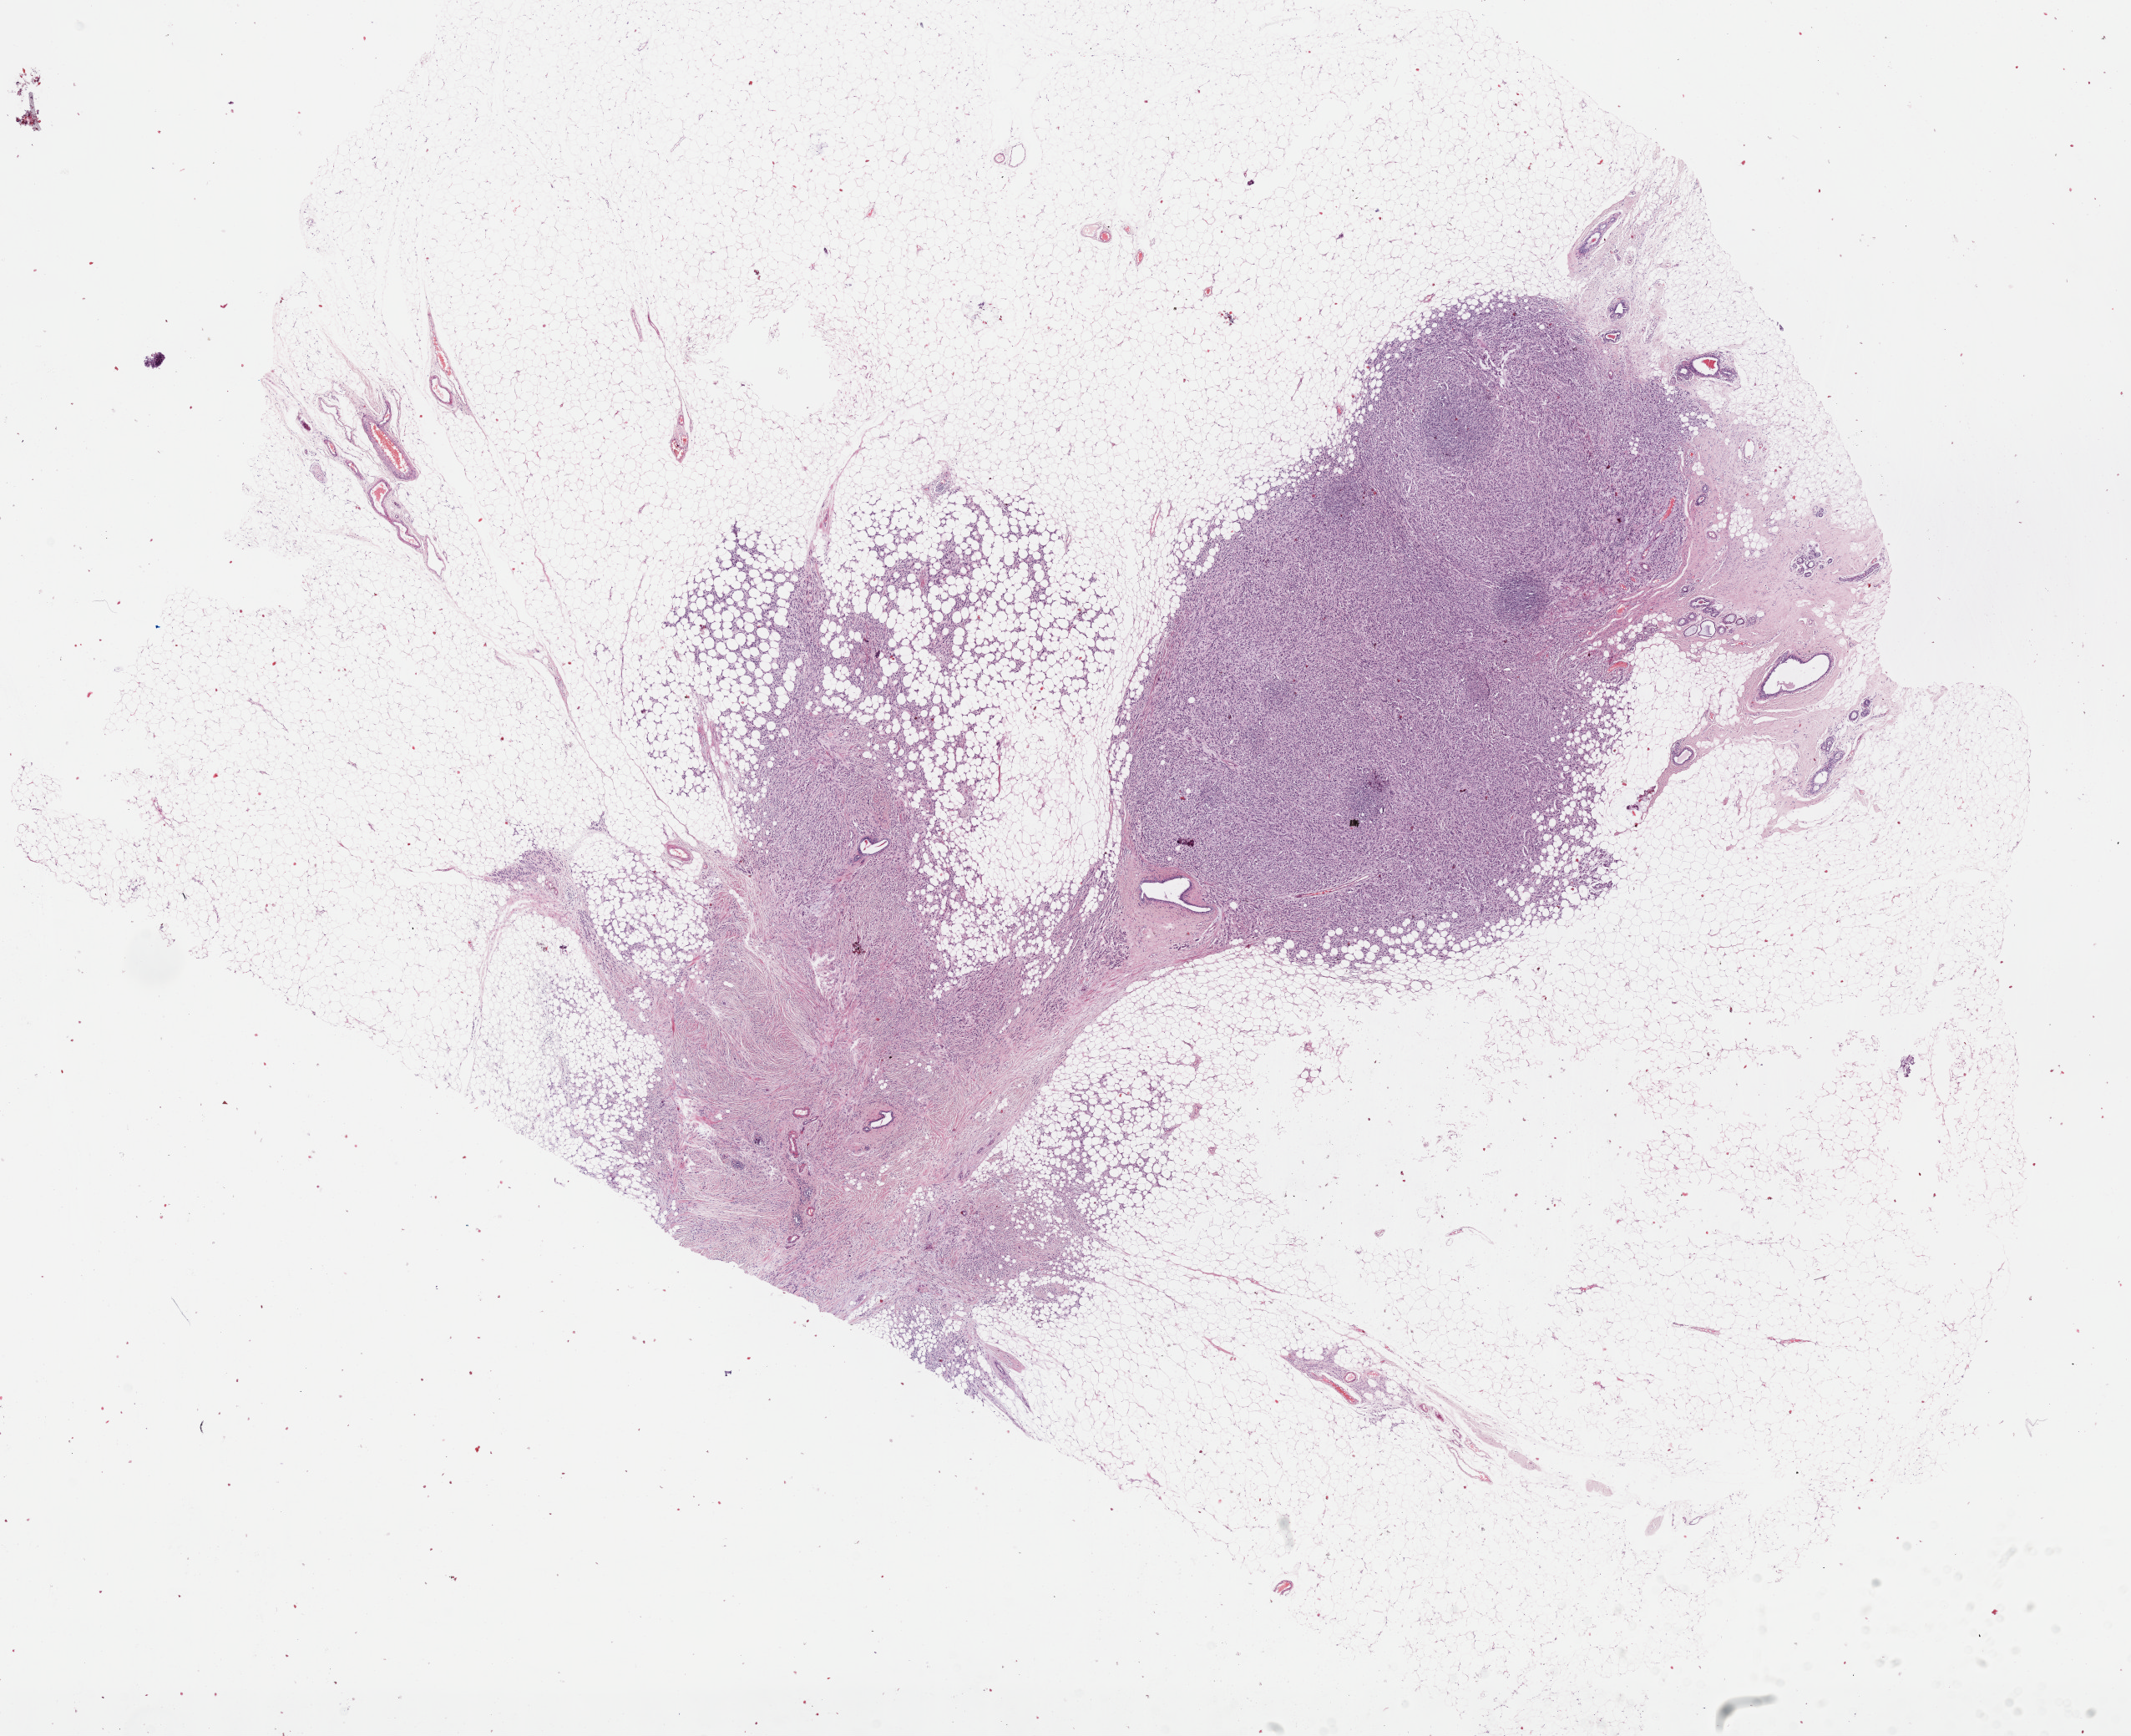
Digitized Hematoxylin and eosin (H&E) stained tissue section (whole slide), low-resolution overview of the scanned area, about 20.6 x 16.8 mm (acquisition: 40x scan). Formalin-fixed paraffin-embedded (FFPE) diagnostic section. Breast, primary tumour sample. Female patient; age at initial diagnosis 62 years.
Lymph nodes positive (case pathology): 0 of 2 examined. TNM: T2 N0 M0. AJCC pathologic stage: IIA (7th edition). Pathologic diagnosis: Lobular carcinoma, NOS.